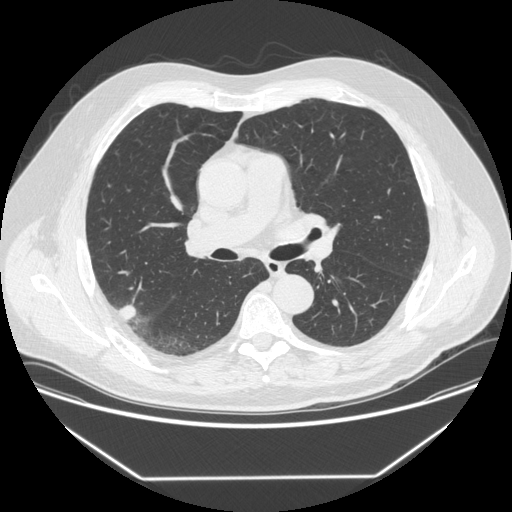
Low-dose screening chest CT, one axial slice. Position 212 of 342 along the scan axis. 120 kVp. Lung window (W 1500 / L -600 HU). 1.25 mm slice thickness. 512 × 512 image matrix, field of view 410 × 410 mm.
Outlined on this slice (manually delineated by an expert):
- lesion 1 (tumor, upper lobe of right lung): bounding box <119,304,137,320> (left, top, right, bottom; pixels)